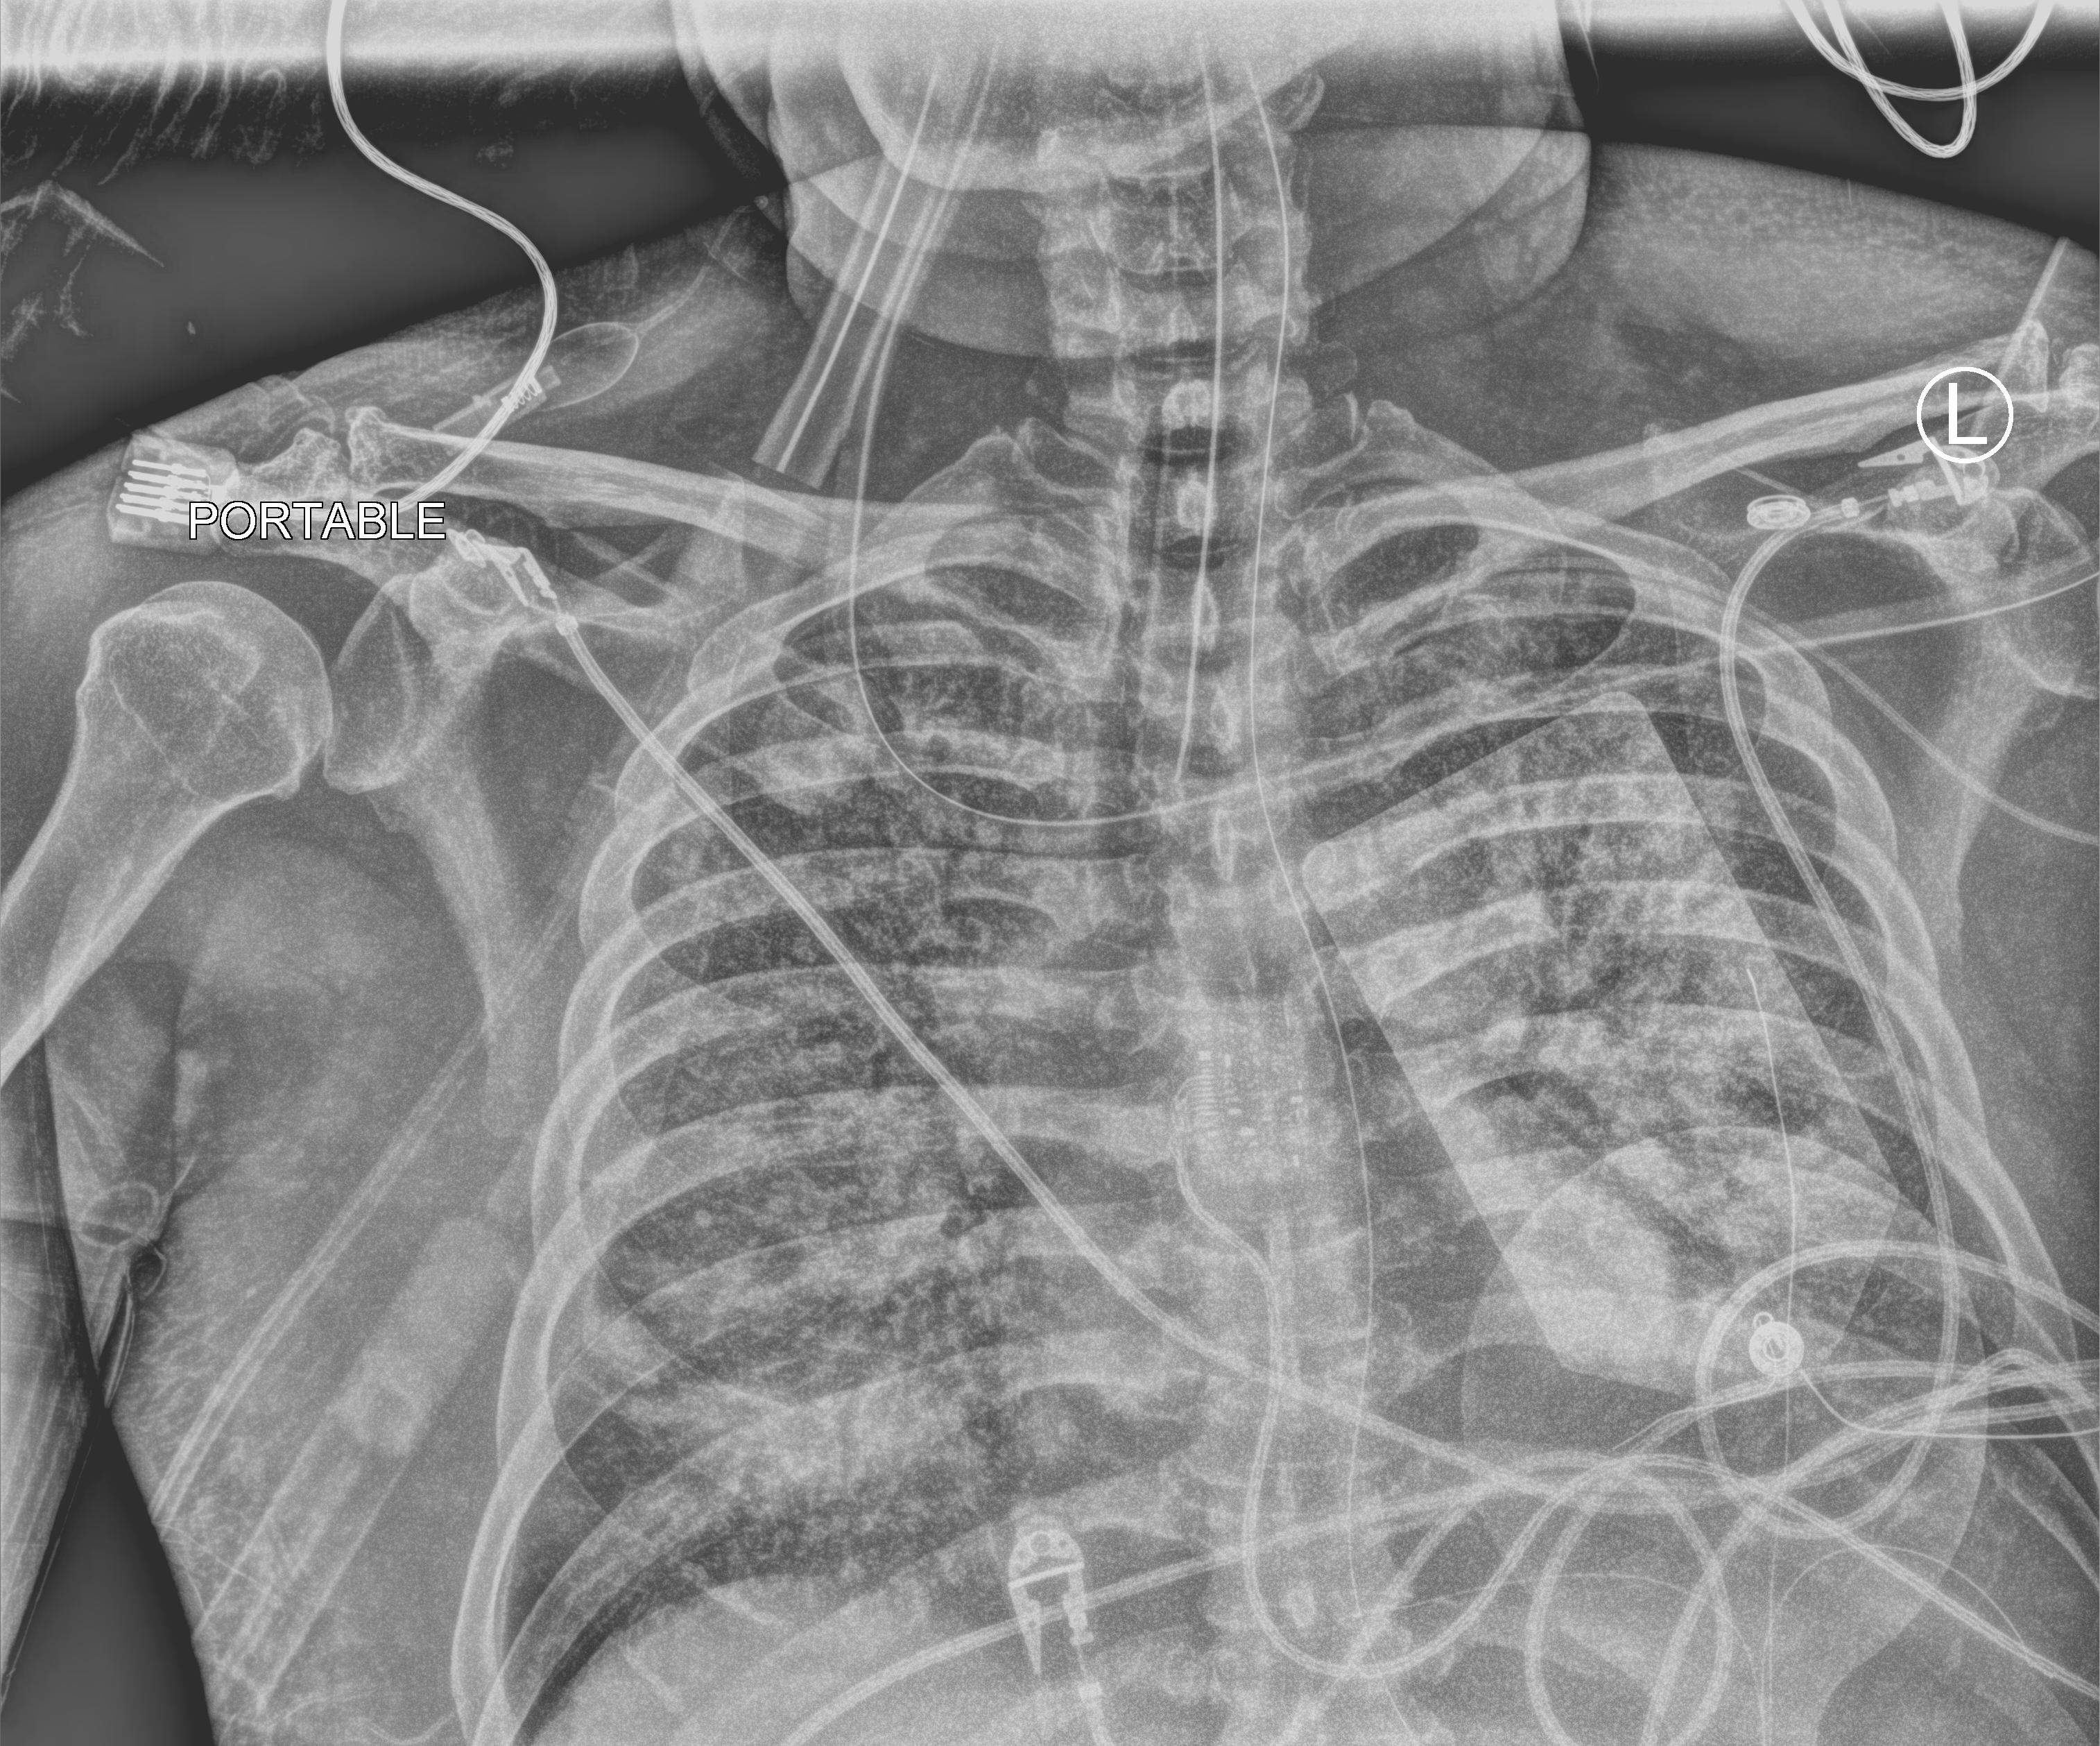
Bedside chest radiograph (computed radiography), anteroposterior (AP) projection. Patient hospitalised with COVID-19; male, aged 60–74 years.
Admission-level facts for this patient (not findings on this image; timing relative to this image not recorded):
- COPD (admission record): no